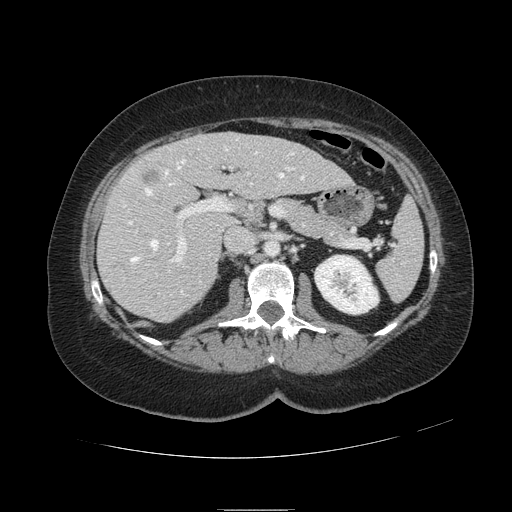
Contrast-enhanced abdominal CT, one axial slice; position 56 of 121 along the scan axis; 120 kVp; intravenous contrast given; soft-tissue window (W 400 / L 40 HU); 512 × 512 image matrix, field of view 400 × 400 mm. Female patient, age 52 years. Case-level facts recorded for this patient, not image findings: diagnosis: colorectal cancer liver metastases, imaged before liver resection.
Structures marked on this image (expert manual segmentation):
- hepatic veins: bounding box (x1, y1, x2, y2) in pixels: (123, 147, 304, 293)
- liver: (99, 133, 350, 322)
- planned liver remnant (the part of the liver to remain after resection): (169, 133, 349, 198)
- portal vein (with intrahepatic branches): (129, 167, 293, 262)
- liver metastasis: (142, 170, 158, 185)